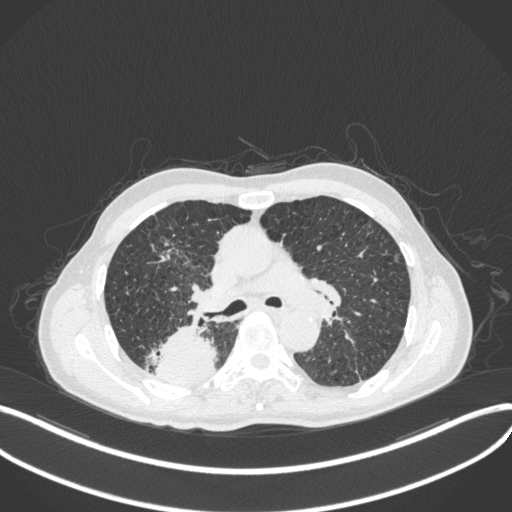
Chest CT, one axial slice. Position 287 of 423 along the scan axis. Reconstruction kernel B31f. Lung window (W 1500 / L -600 HU). 1 mm slice thickness. 512 × 512 image matrix. Male patient, age 79 years. Case-level facts recorded for this patient, not image findings: clinical TNM (as recorded): T3 N0 M0.
Outlined on this slice (rectangle marked by the reading radiologist):
- lung tumour (recorded histology: adenocarcinoma): box from (x=152, y=323) to (x=219, y=391) px